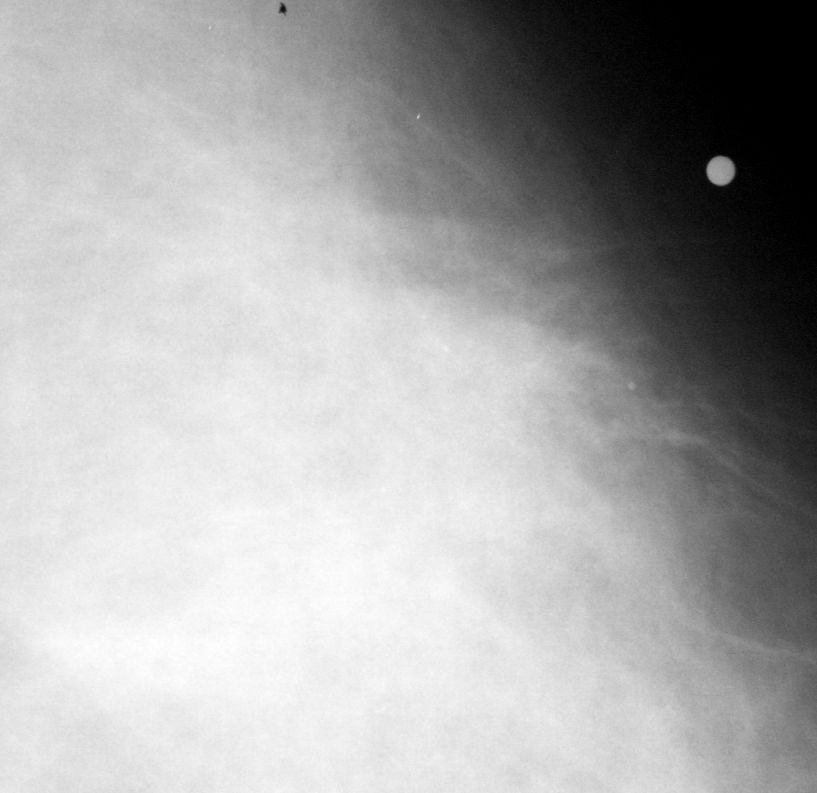
Region of interest cut from a scanned film mammogram (one marked finding); left breast; CC view; BI-RADS breast density category 2 (scale 1–4).
- Marked abnormality: calcifications, morphology amorphous, distribution clustered; BI-RADS assessment category 4; subtlety rating 2 on a 1 (subtle) to 5 (obvious) scale; pathology (as recorded): malignant.